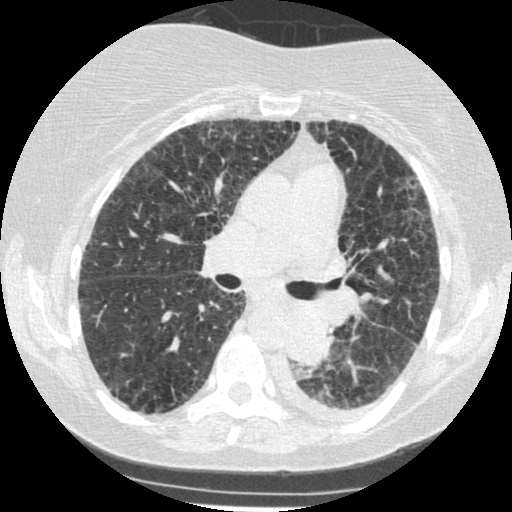
Low-dose screening chest CT, one axial slice. Position 150 of 341 along the scan axis. Reconstruction kernel STANDARD. 120 kVp. Lung window (W 1500 / L -600 HU). 1.25 mm slice thickness. 512 × 512 image matrix, field of view 310 × 310 mm.
Outlined on this slice (outlined manually by an expert reader):
- lesion 1 (tumor, lower lobe of left lung): bounding box <287,309,333,366> (left, top, right, bottom; pixels)